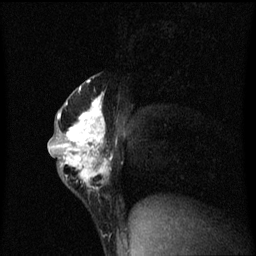
Breast MRI (dynamic contrast-enhanced), one sagittal slice. Position 34 of 60 along the scan axis. Dynamic contrast-enhanced series, image 2 of 3 at this slice position (ordered by acquisition). 1.5 T. TE 4.2 ms, TR 8.4 ms. 256 × 256 image matrix, field of view 200 × 200 mm. Patient: female, 40 years.
Structures marked on this image (semi-automatically segmented with operator editing):
- analysis volume of interest (the breast-tissue region the enhancement analysis was run in; not a lesion): box from (x=49, y=74) to (x=113, y=201) px
- tumour enhancement mask (voxels above the 70 % enhancement threshold inside the analysis volume of interest): (x=49, y=80)–(x=113, y=191)